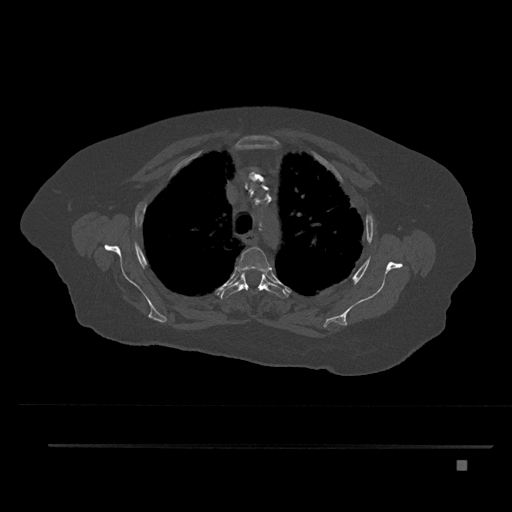
CT including the spine, one axial slice; reconstruction kernel Br40s/3; 120 kVp; bone window (W 1800 / L 400 HU); 512 × 512 image matrix, field of view 437 × 437 mm. Patient: female, 76 years. Case-level facts recorded for this patient, not image findings: primary cancer: lung.
Structures marked on this image (semi-automatically segmented with operator editing):
- T3 vertebra: box from (x=237, y=247) to (x=271, y=272) px
- T4 vertebra: (x=220, y=269)–(x=289, y=299)